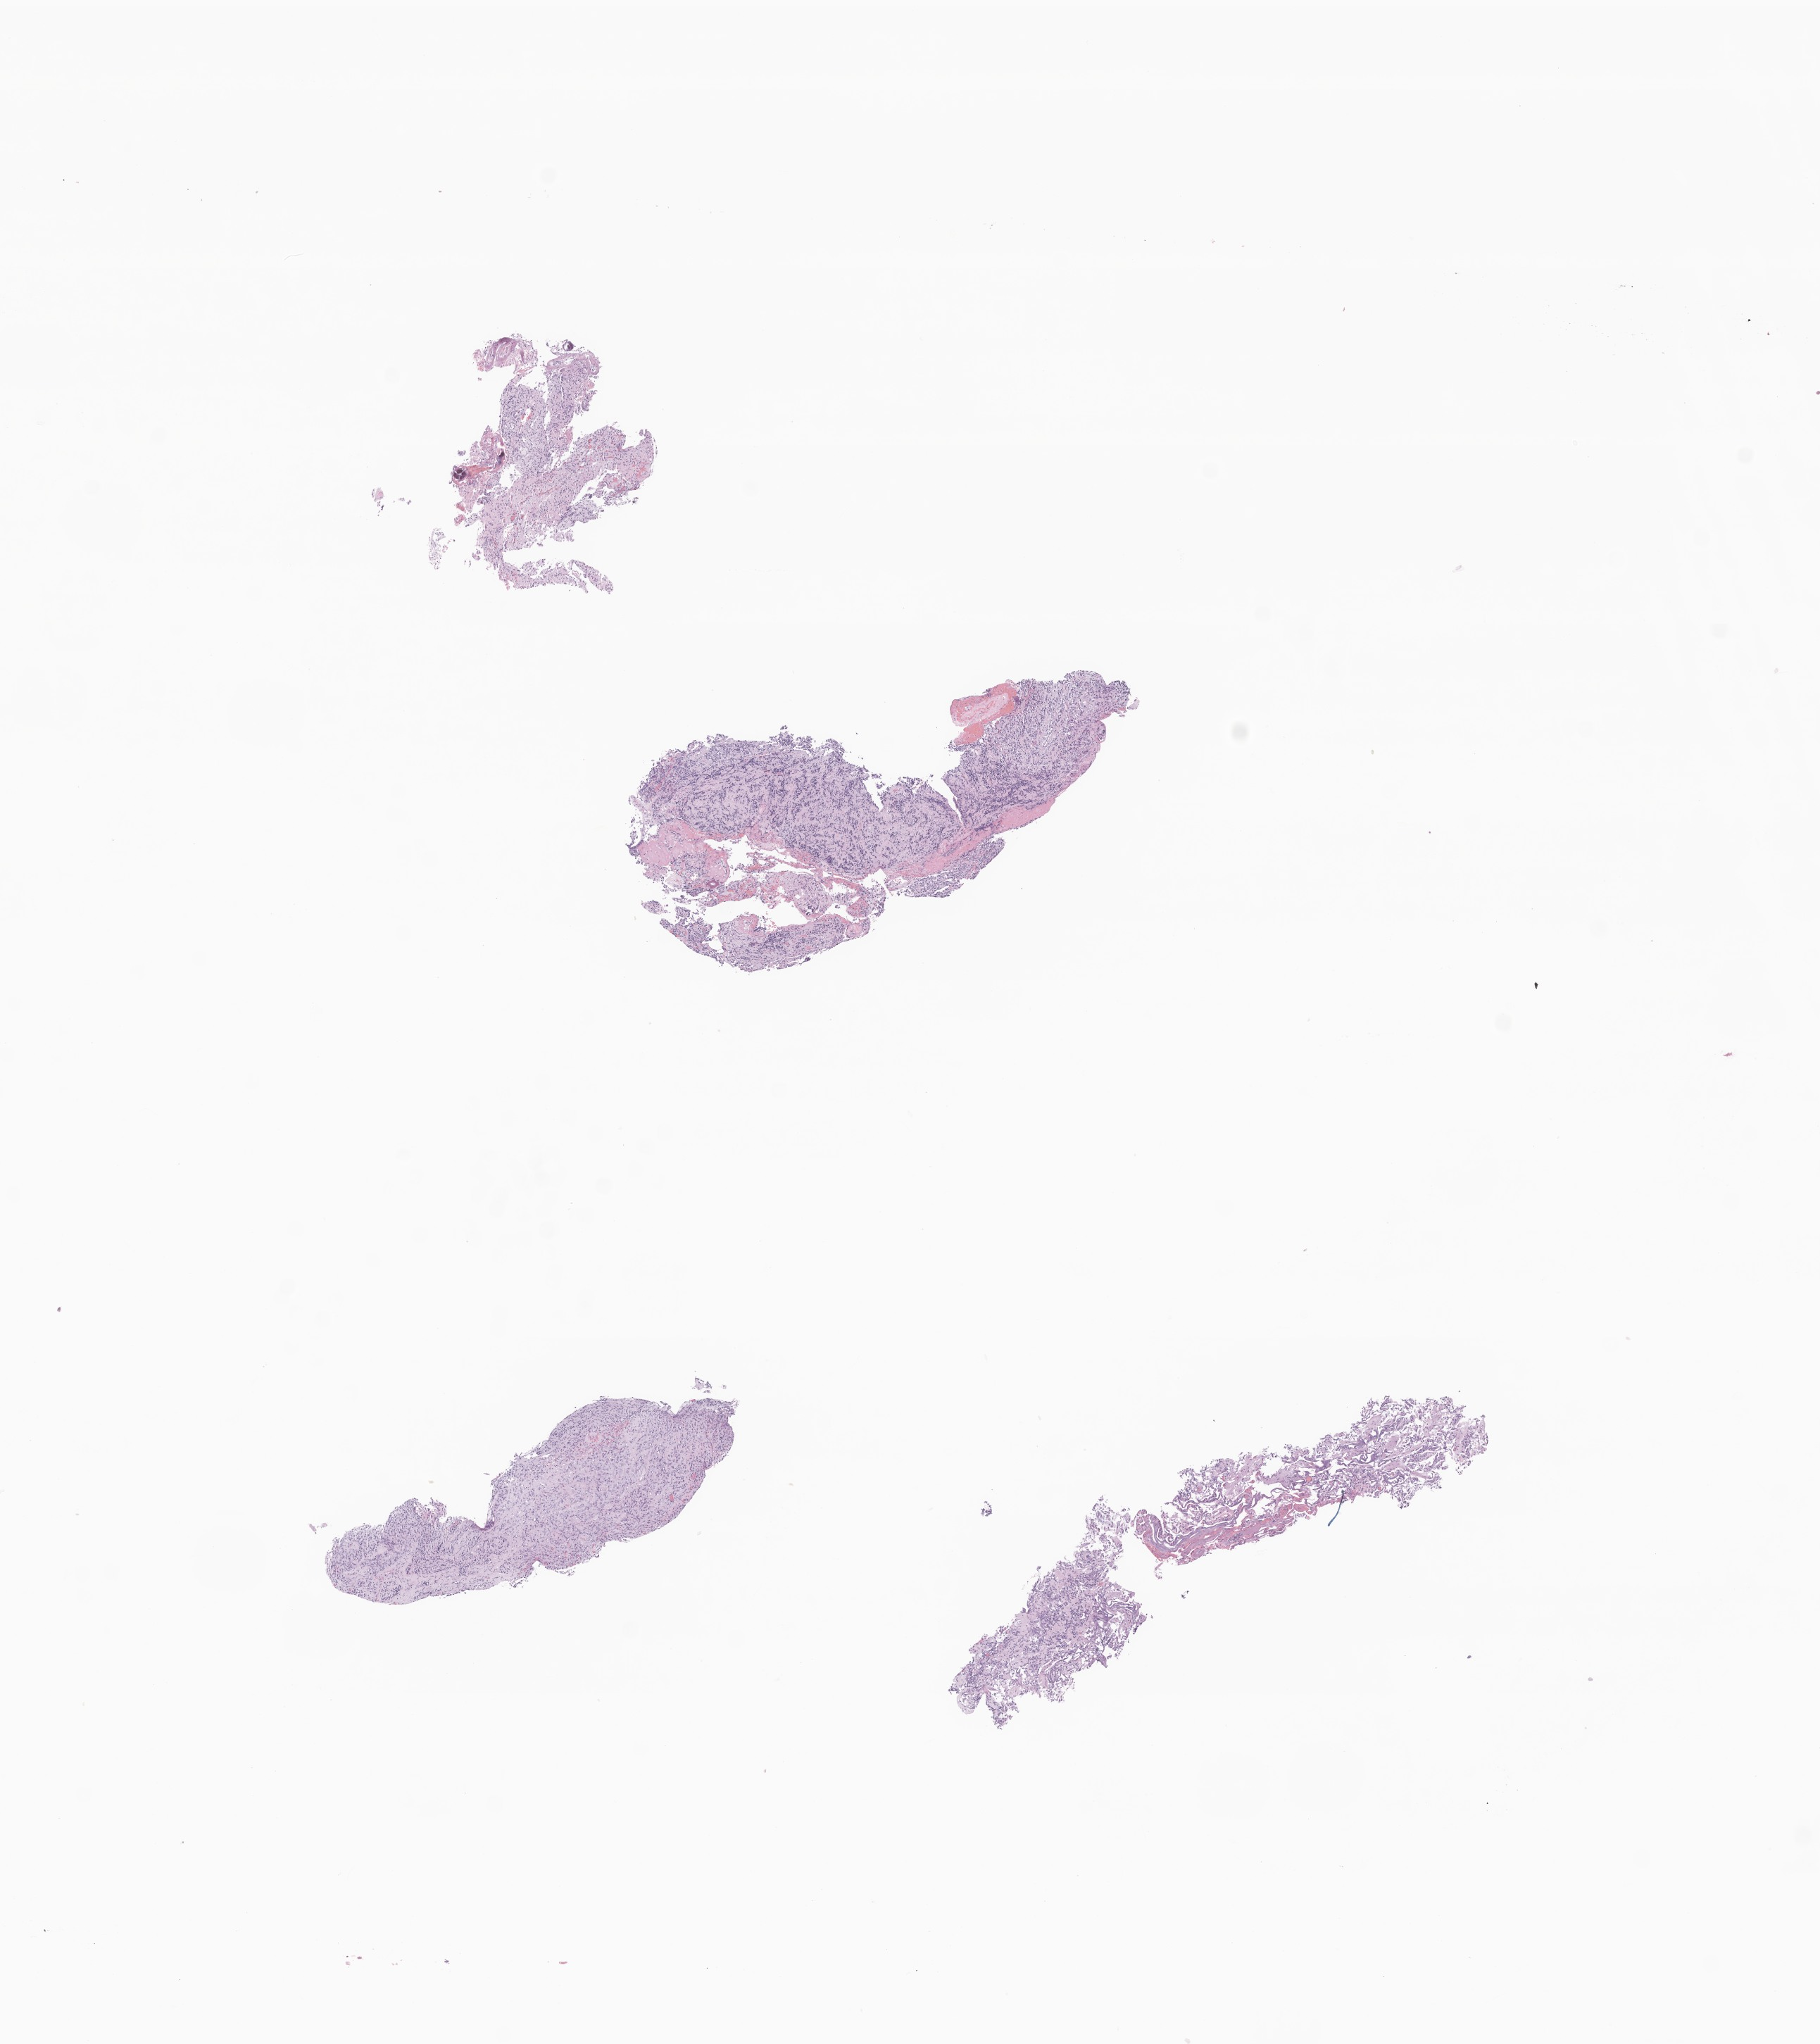
Digitized H&E-stained section of tumor tissue from the pineal gland — shown as a low-resolution overview of the whole scanned area (about 10.9 x 12.2 mm), formalin-fixed paraffin-embedded section. Patient: male, age 220 months (18 years 4 months).
Diagnosis (ICD-O-3 morphology term): Neoplasm, uncertain whether benign or malignant.